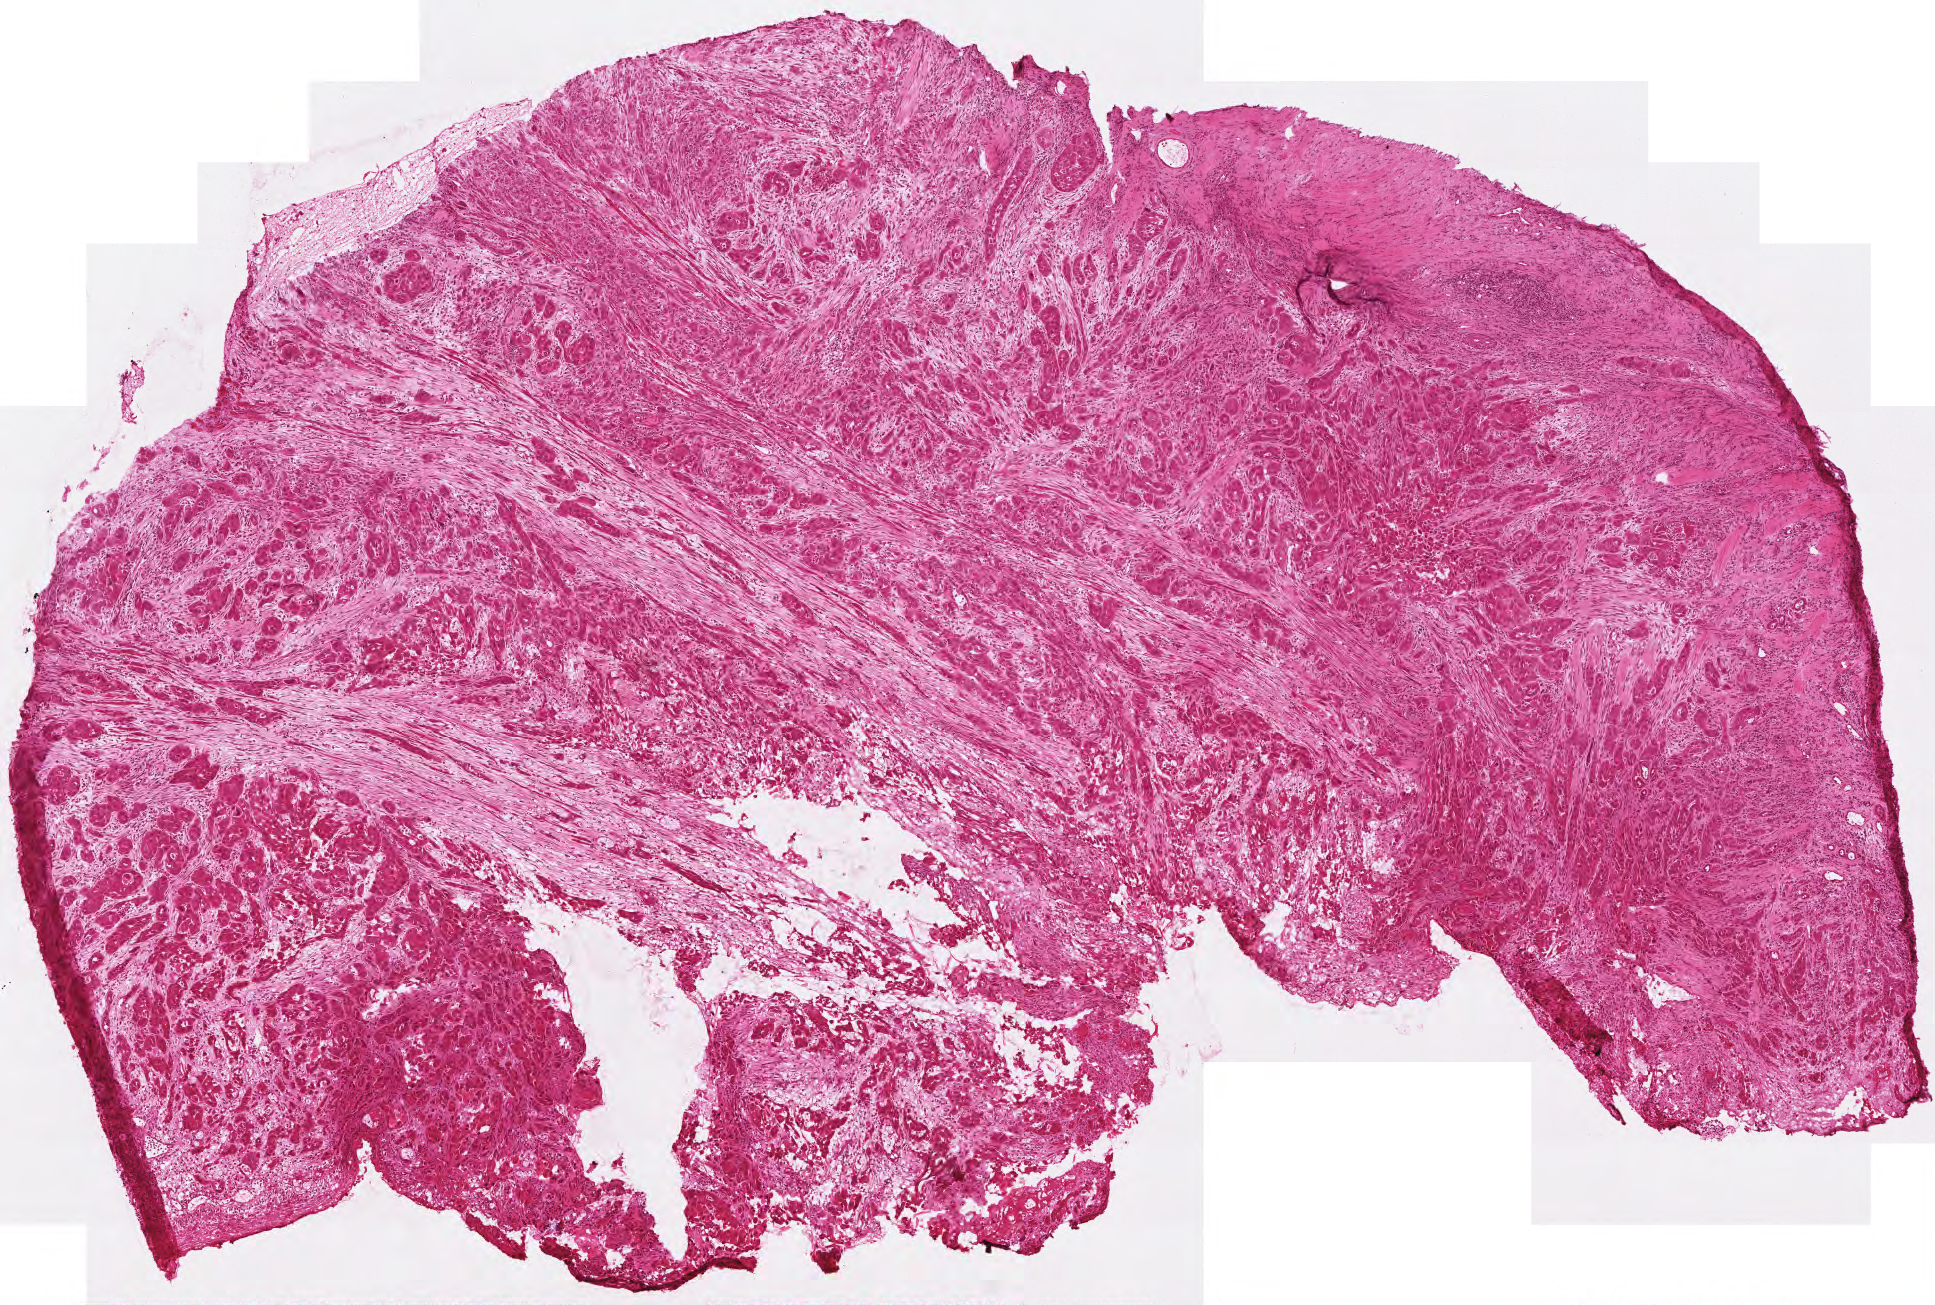
Hematoxylin and eosin (H&E) stained whole-slide image — shown as a low-resolution overview of the whole scanned area (about 3.9 x 2.6 mm), frozen section from the top of the tissue portion, head and neck, primary tumour sample. Patient: male, age at initial diagnosis 51 years. Histologic grade: G2 (moderately differentiated). Pathologist review of this section (percent, as recorded): tumour cells 85%, tumour nuclei 85%, normal cells 0%, stromal cells 15%, necrosis 0%.
Lymph nodes positive (case pathology): 2 of 31 examined. AJCC pathologic stage: IVA (6th edition). Diagnosis: Squamous cell carcinoma, NOS (larynx, NOS). Laterality: left.